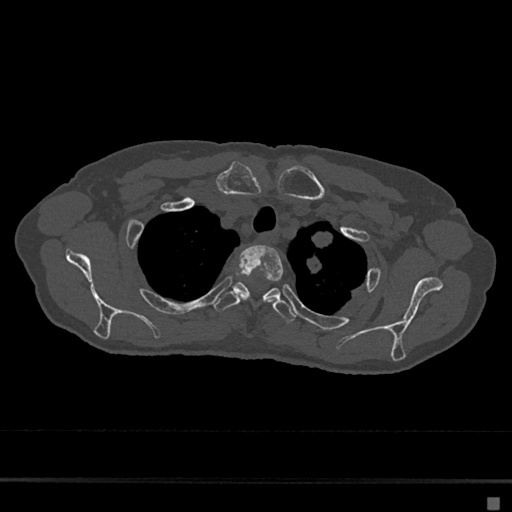
CT including the spine, one axial slice; slice 559 of 797 in the series (ordered by position); 120 kVp; bone window (W 1800 / L 400 HU); 512 × 512 image matrix. Patient: female, 68 years. Case-level facts recorded for this patient, not image findings: primary cancer: renal.
Structures marked on this image (semi-automatic segmentation, software-assisted and operator-edited):
- T2 vertebra: bounding box <239,245,283,302> (left, top, right, bottom; pixels)
- T3 vertebra: <212,282,296,323>